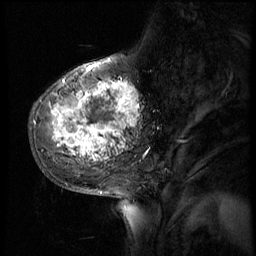
Breast MRI (dynamic contrast-enhanced), one sagittal slice; position 18 of 56 along the scan axis; 4 images stored at this slice position (order not interpretable as contrast timing); 1.5 T; TE 4.2 ms, TR 8.9 ms; 2.5 mm slice thickness; 256 × 256 image matrix. Female patient, age 51 years. Case-level facts recorded for this patient, not image findings: setting: breast cancer imaged before/during neoadjuvant chemotherapy; receptor status: triple-negative.
Outlined on this slice (semi-automatically segmented with operator editing):
- analysis volume of interest (the breast-tissue region the enhancement analysis was run in; not a lesion): bounding box (x1, y1, x2, y2) in pixels: (30, 70, 150, 173)
- tumour enhancement mask (voxels above the 140 % enhancement threshold inside the analysis volume of interest): (53, 70, 140, 161)